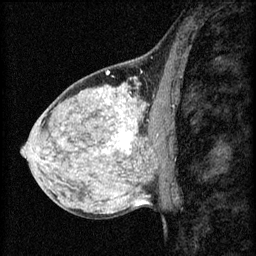
Breast MRI (dynamic contrast-enhanced), one sagittal slice. Position 33 of 60 along the scan axis. 3 images stored at this slice position (order not interpretable as contrast timing). 1.5 T. TE 4.2 ms, TR 8.2 ms. 256 × 256 image matrix, field of view 180 × 180 mm. Patient: female, 40 years.
Annotated regions visible in this slice (semi-automatically segmented with operator editing):
- analysis volume of interest (the breast-tissue region the enhancement analysis was run in; not a lesion): bounding box <108,108,167,159> (left, top, right, bottom; pixels)
- tumour enhancement mask (voxels above the 70 % enhancement threshold inside the analysis volume of interest): <108,118,159,153>